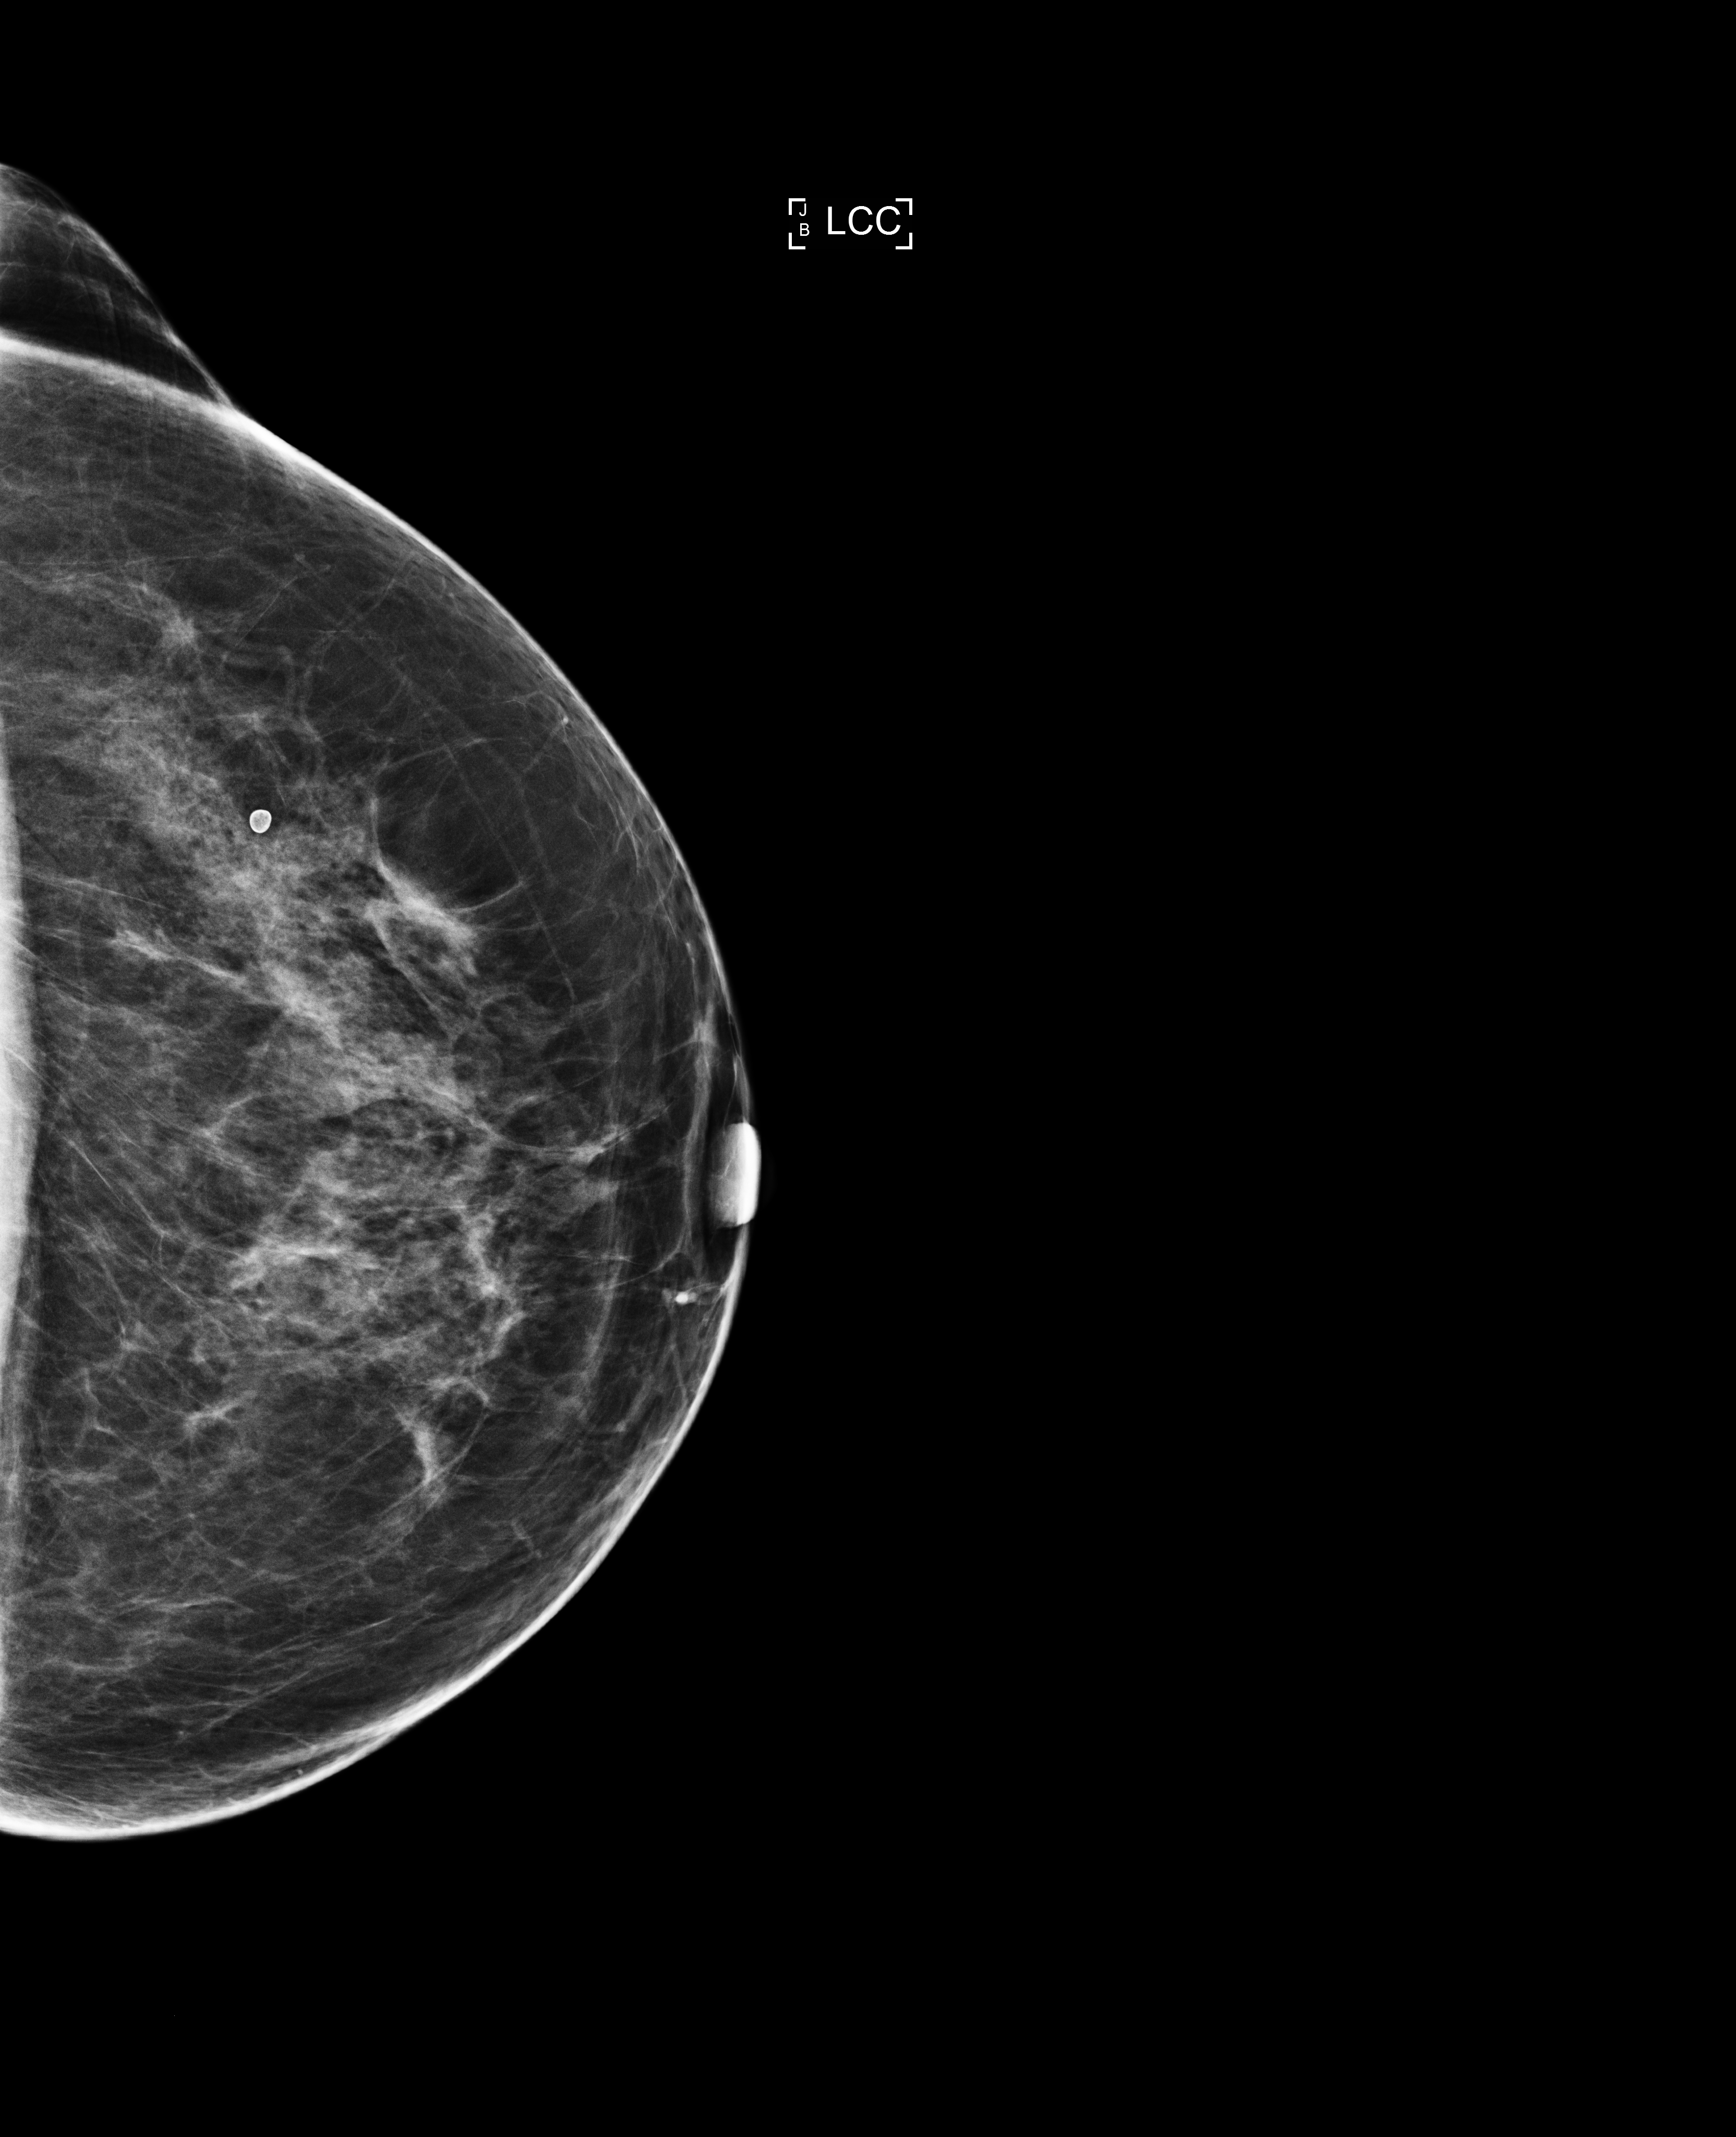
Digital mammogram (FFDM); left breast; CC view; annual screening mammography examination; compressed breast thickness 68 mm. Patient: female, 63 years.
BI-RADS breast density category at the screening exam (both breasts, scale 1–4): 2. Final BI-RADS assessment for this screening round (tomosynthesis exam, both breasts): category 1. Recall: no recall after this screen.